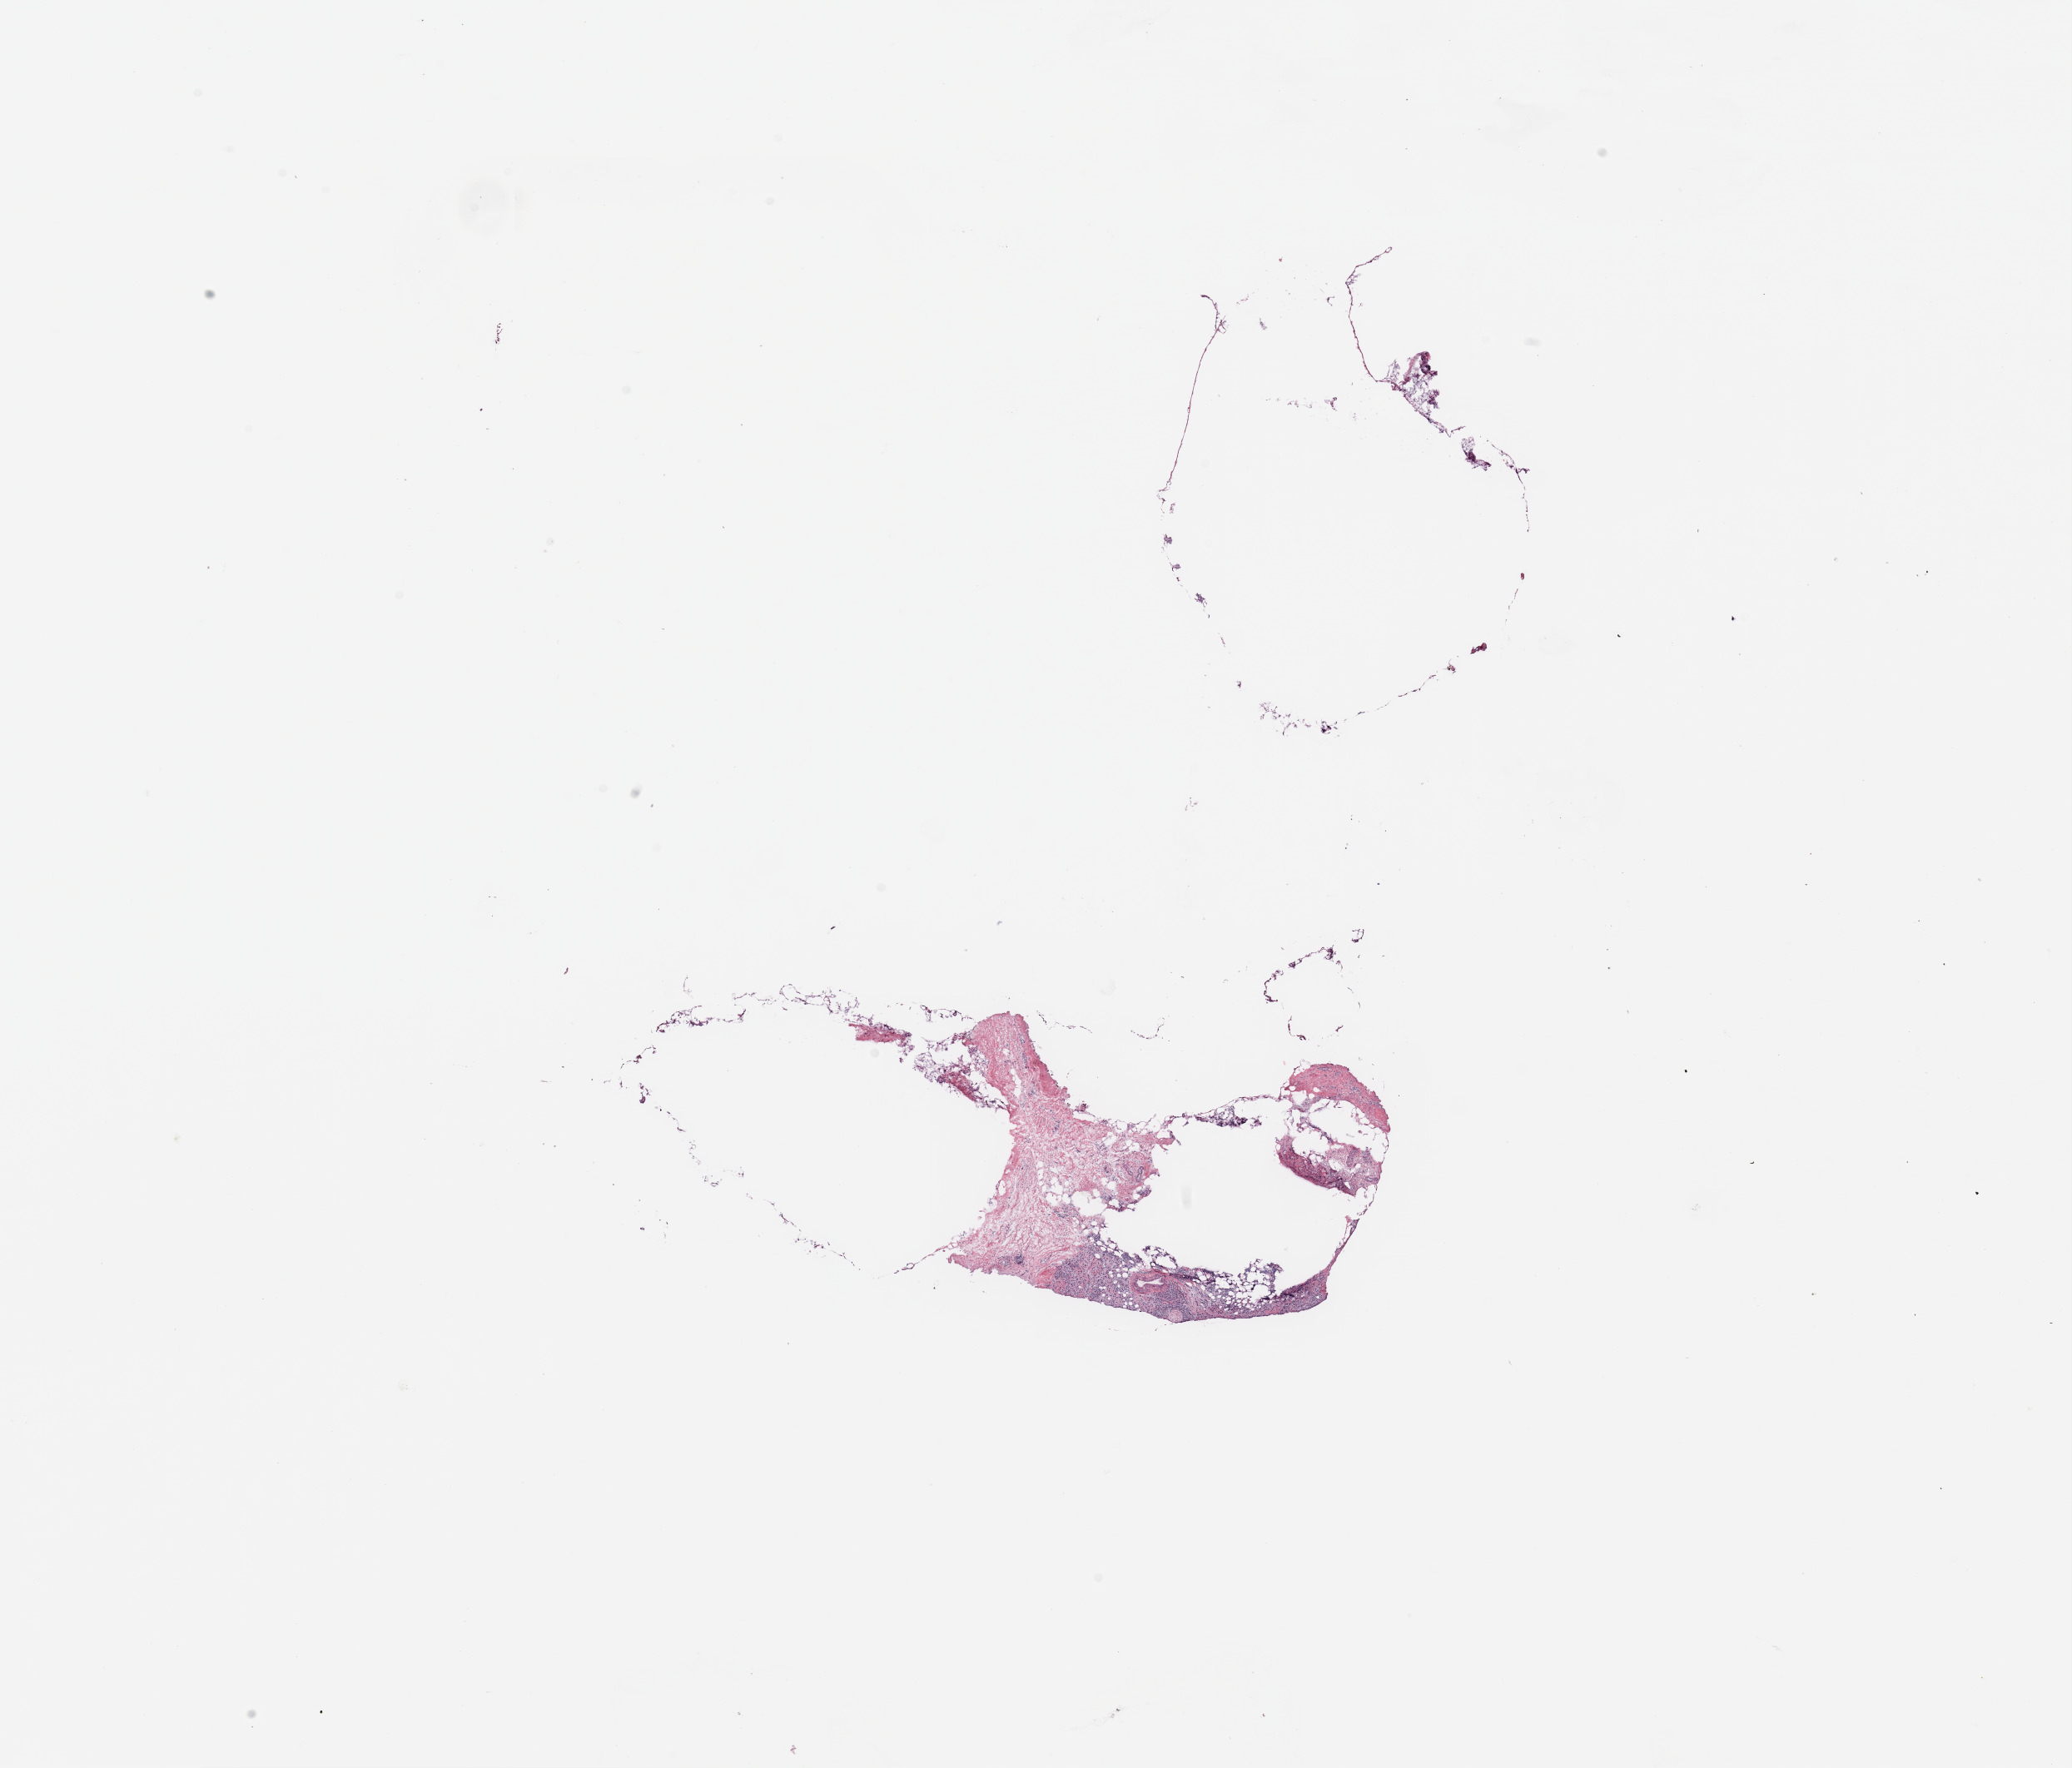
Digitized Hematoxylin and eosin (H&E) stained tissue section (whole slide), whole scanned area (about 19.7 x 16.8 mm) shown as a low-resolution overview. Breast, tissue type not recorded.
Patient diagnosis (cohort enrolment): breast cancer (breast).